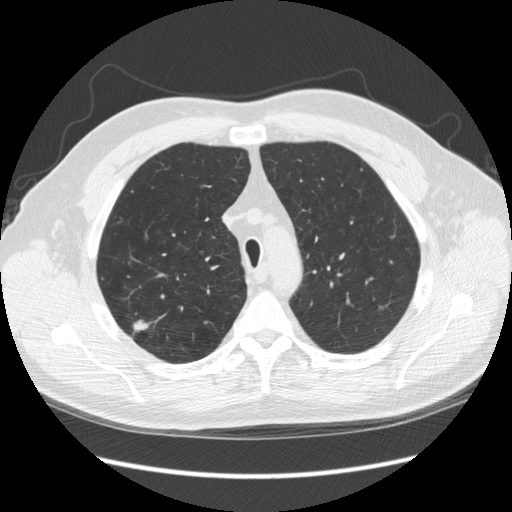
Low-dose screening chest CT, one axial slice. Slice 192 of 248 in the series (ordered by position). Reconstruction kernel STANDARD. 120 kVp. Lung window (W 1500 / L -600 HU). 2.5 mm slice thickness. 512 × 512 image matrix.
Outlined on this slice (expert manual segmentation):
- lesion 1 (tumor, upper lobe of right lung): bounding box <133,320,148,331> (left, top, right, bottom; pixels)